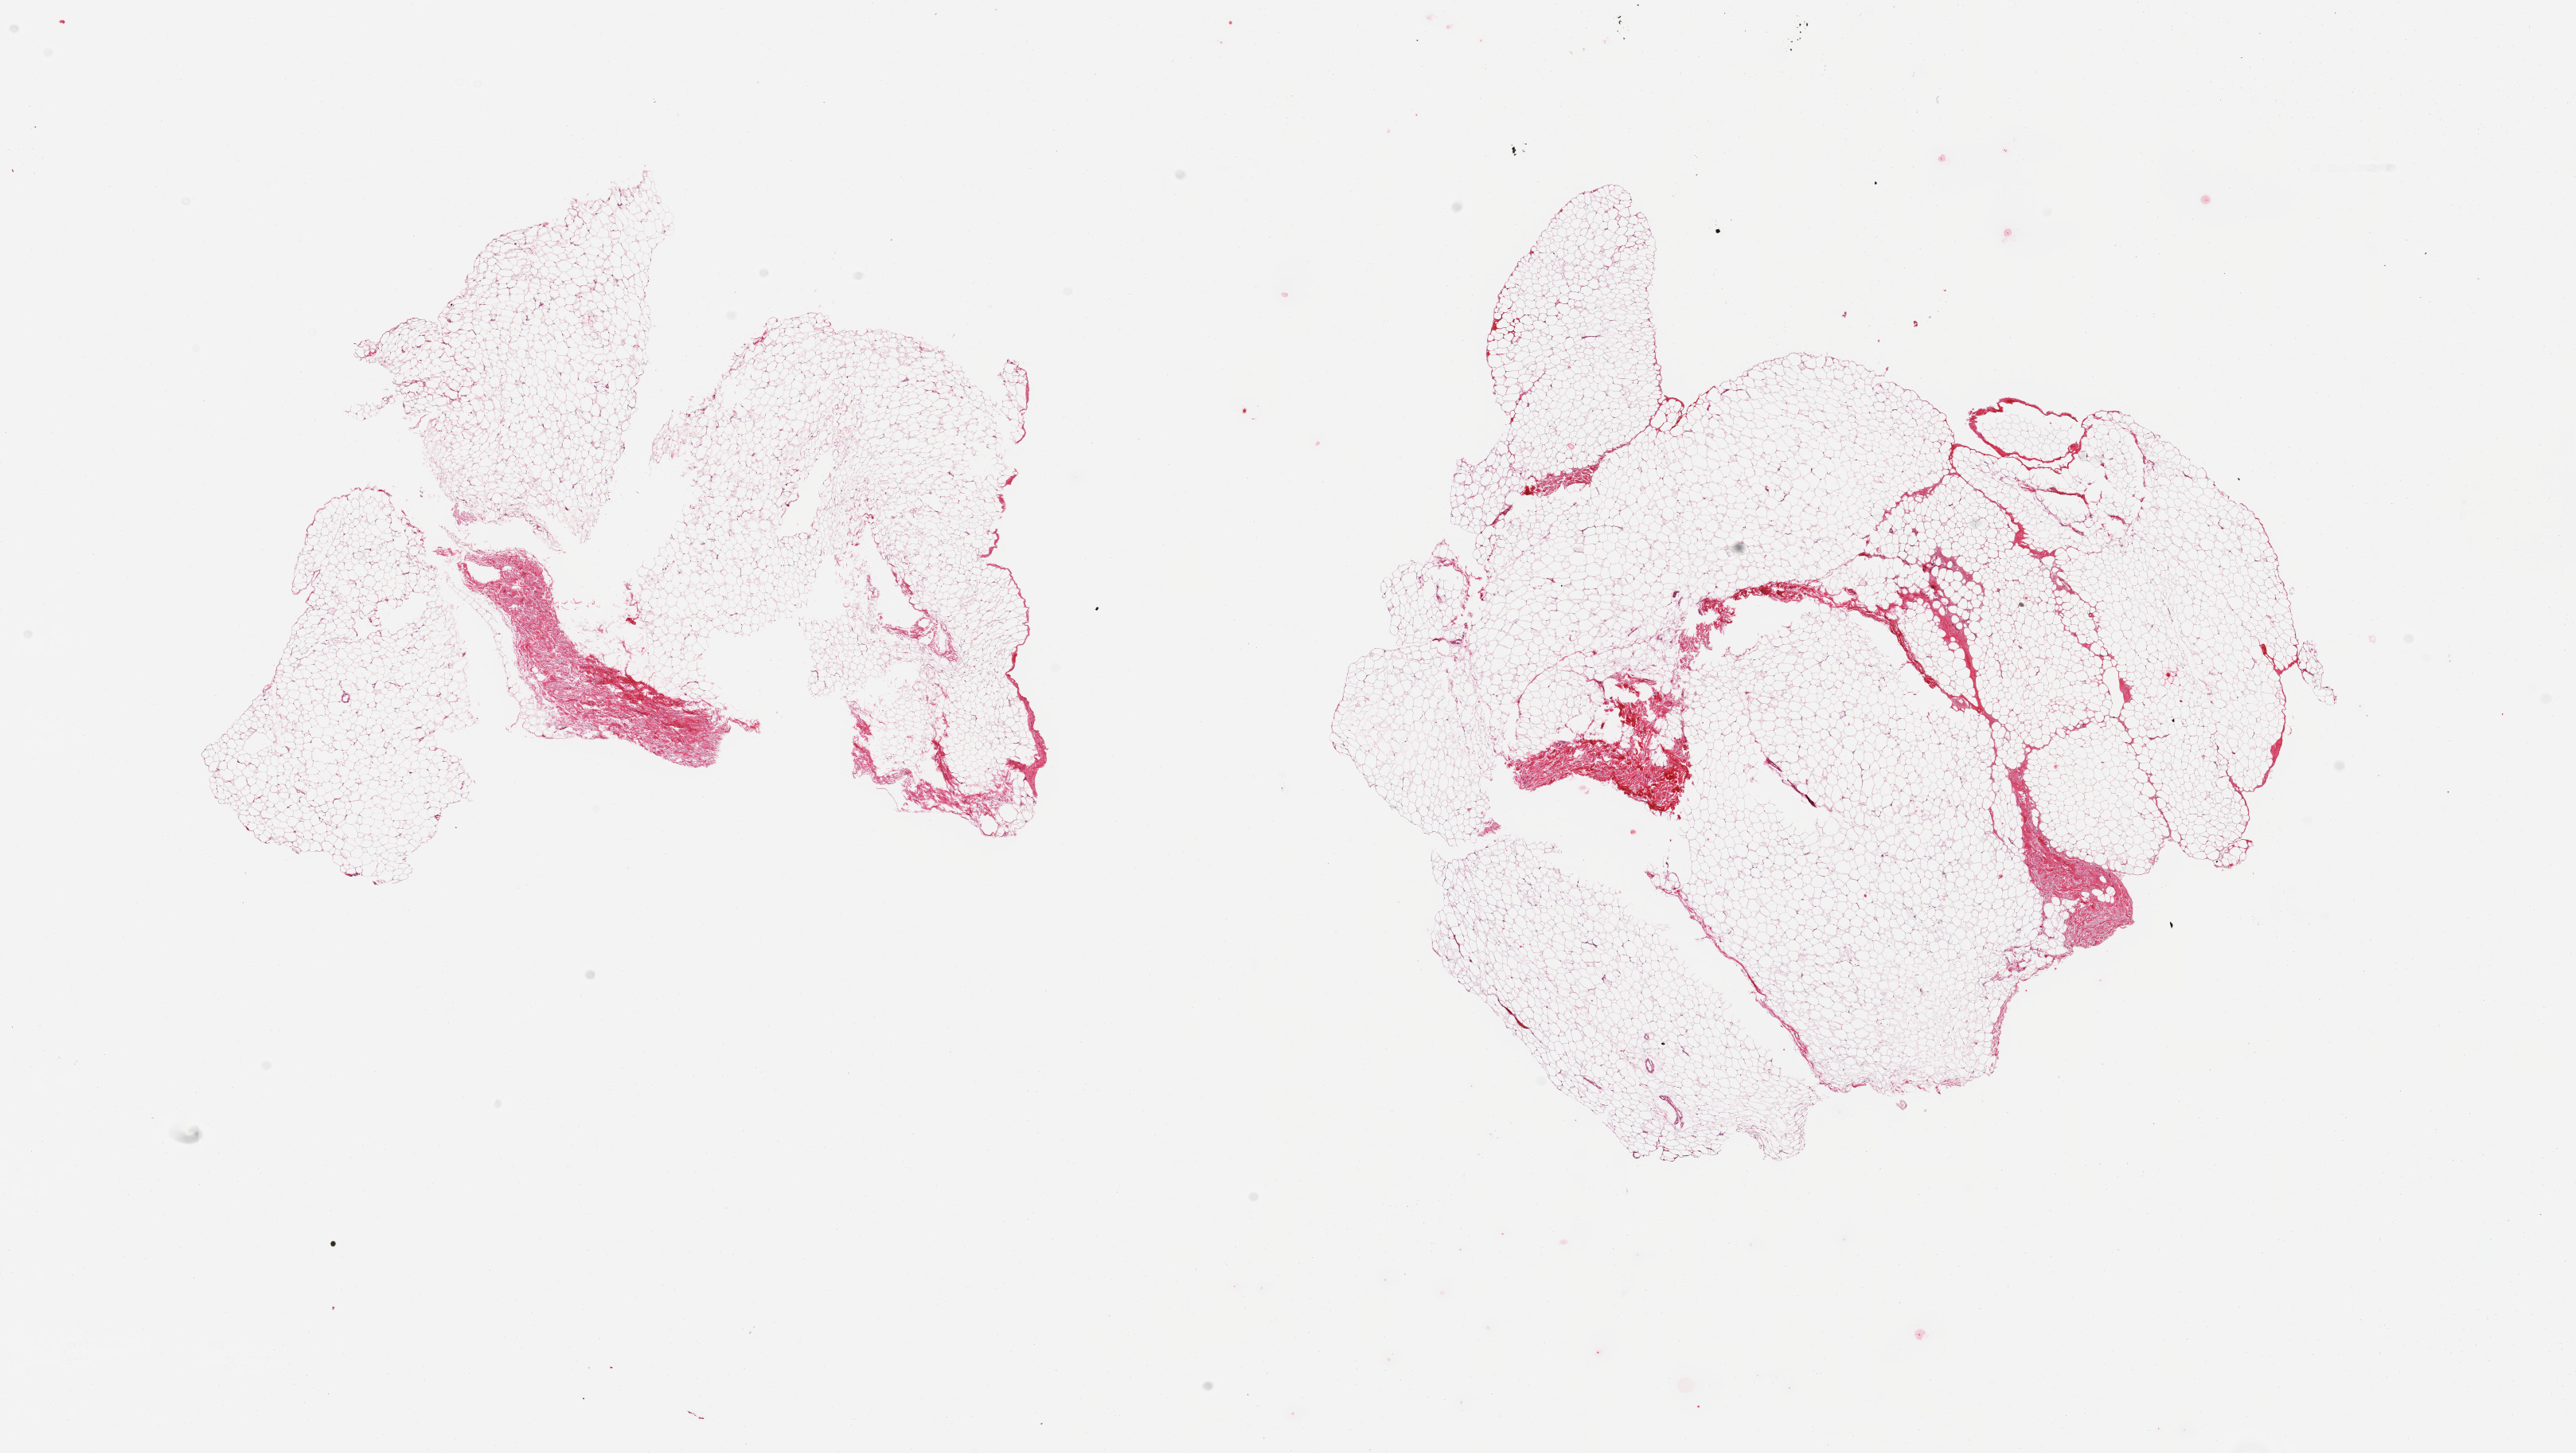
Digitized H&E-stained section — a low-resolution overview of the entire scanned area, about 25.6 x 14.4 mm. PAXgene-fixed, paraffin-embedded tissue. Sampled site (target tissue): adipose tissue. Tissue donor sample. Male donor.
Review note (as recorded): 2 pieces, ~10 % fascia.